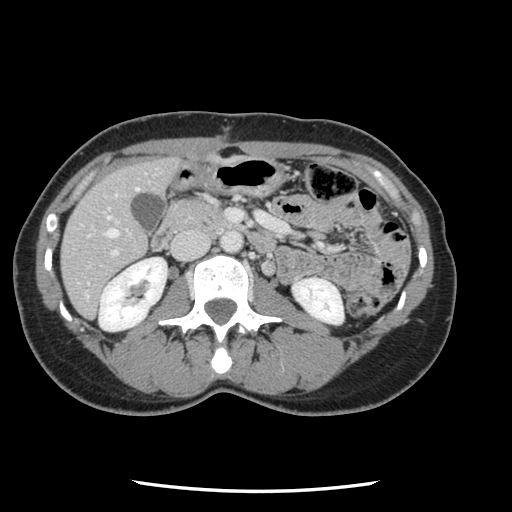
Contrast-enhanced abdominal CT, one axial slice. Slice 37 of 134 in the series (ordered by position). 120 kVp. Intravenous contrast given. Soft-tissue window (W 400 / L 40 HU). 512 × 512 image matrix, field of view 330 × 330 mm. Female patient, age 43 years. From the clinical record (not read from this slice): diagnosis: colorectal cancer liver metastases, imaged before liver resection; multiple liver metastases: yes; largest metastasis: 3.4 cm; chemotherapy before resection: no.
Structures marked on this image (manually delineated by an expert):
- hepatic veins: bounding box <106,188,139,238> (left, top, right, bottom; pixels)
- liver: <62,159,178,317>
- planned liver remnant (the part of the liver to remain after resection): <62,159,178,317>
- portal vein (with intrahepatic branches): <81,209,278,257>